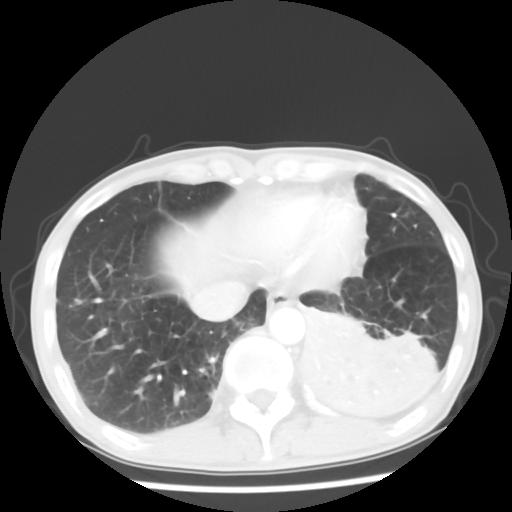
Chest CT, one axial slice. Slice 15 of 64 in the series (ordered by position). Lung window (W 1500 / L -600 HU). 512 × 512 image matrix, field of view 313 × 313 mm. Patient: male, 68 years. From the clinical record (not read from this slice): clinical TNM (as recorded): T4 N0 M0.
Structures marked on this image (rectangle marked by the reading radiologist):
- lung tumour (recorded histology: squamous cell carcinoma): bounding box <283,302,442,437> (left, top, right, bottom; pixels)